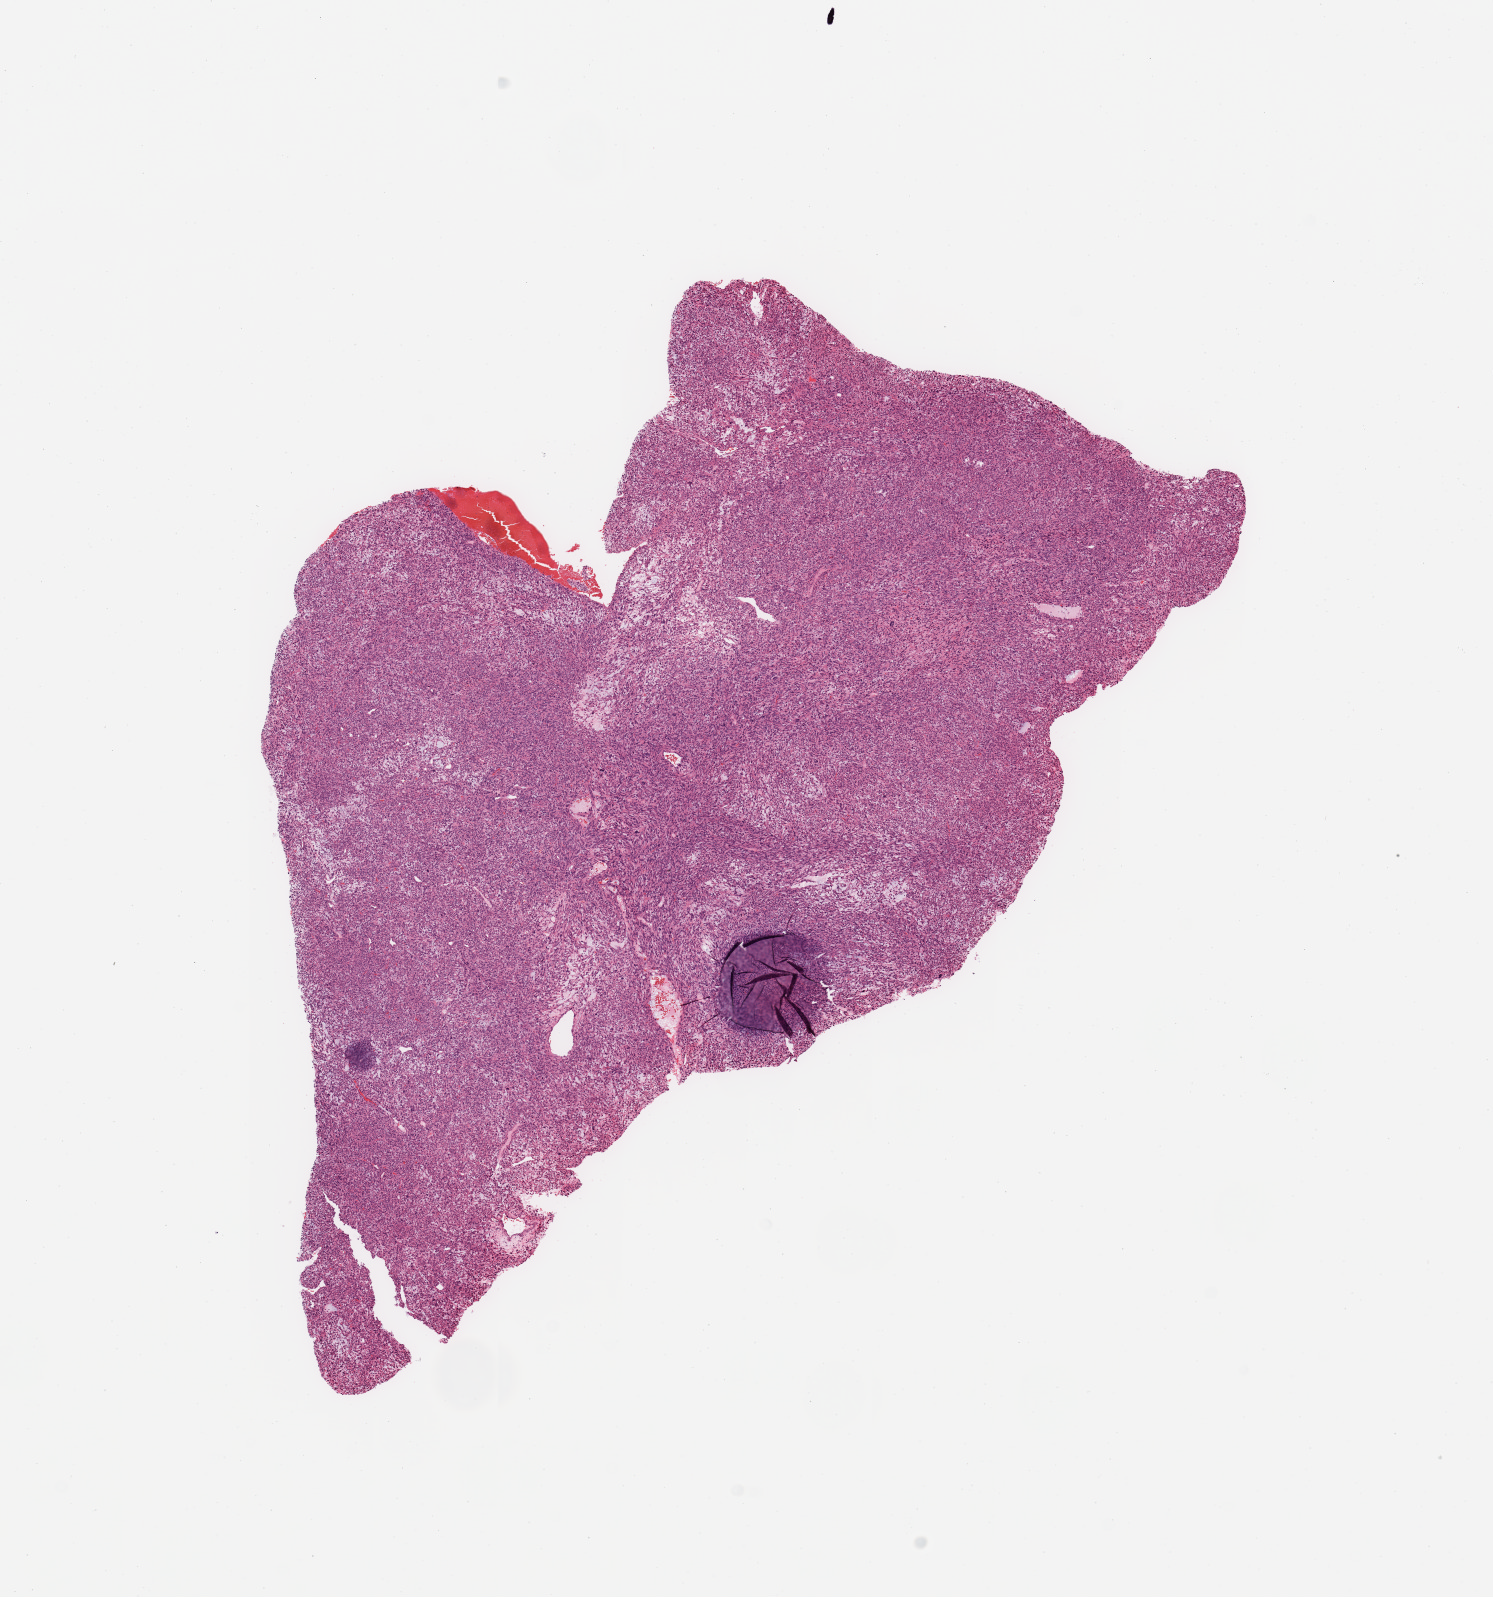
Hematoxylin and eosin (H&E) stained whole-slide image — low-resolution overview of the scanned area, about 11.8 x 12.6 mm (acquisition: 20x scan). Patient: male, age 68 years.
* patient diagnosis (cohort enrolment): sarcoma (site not recorded at cohort level)